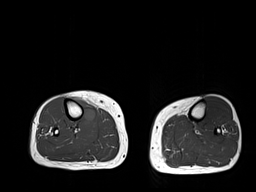
MRI of an extremity soft-tissue mass, one axial slice. Position 15 of 32 along the scan axis. 6 mm slice thickness. 256 × 192 image matrix. Female patient. Case-level facts recorded for this patient, not image findings: histological type: undifferentiated – high grade; grade: high; site of the primary tumour: right thigh.
Annotated regions visible in this slice (expert manual segmentation):
- gross tumour volume (mass): bounding box [x1, y1, x2, y2] px = [71, 95, 96, 125]